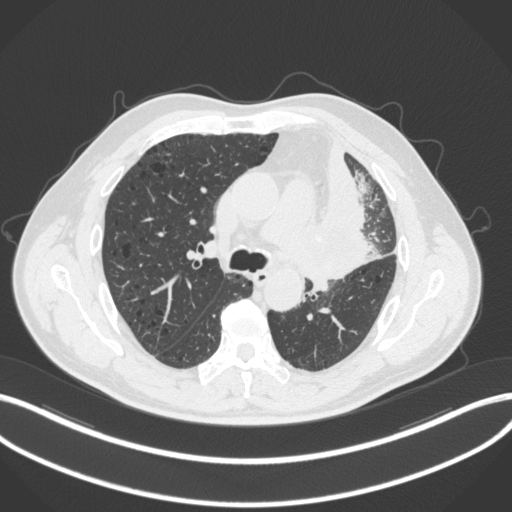
Chest CT, one axial slice. Position 183 of 286 along the scan axis. Reconstruction kernel B31f. 120 kVp. Lung window (W 1500 / L -600 HU). 512 × 512 image matrix, field of view 400 × 400 mm. Male patient, age 68 years. From the clinical record (not read from this slice): clinical TNM (as recorded): T3 N3 M1.
Structures marked on this image (rectangle marked by the reading radiologist):
- lung tumour (recorded histology: adenocarcinoma): box from (x=311, y=193) to (x=380, y=284) px